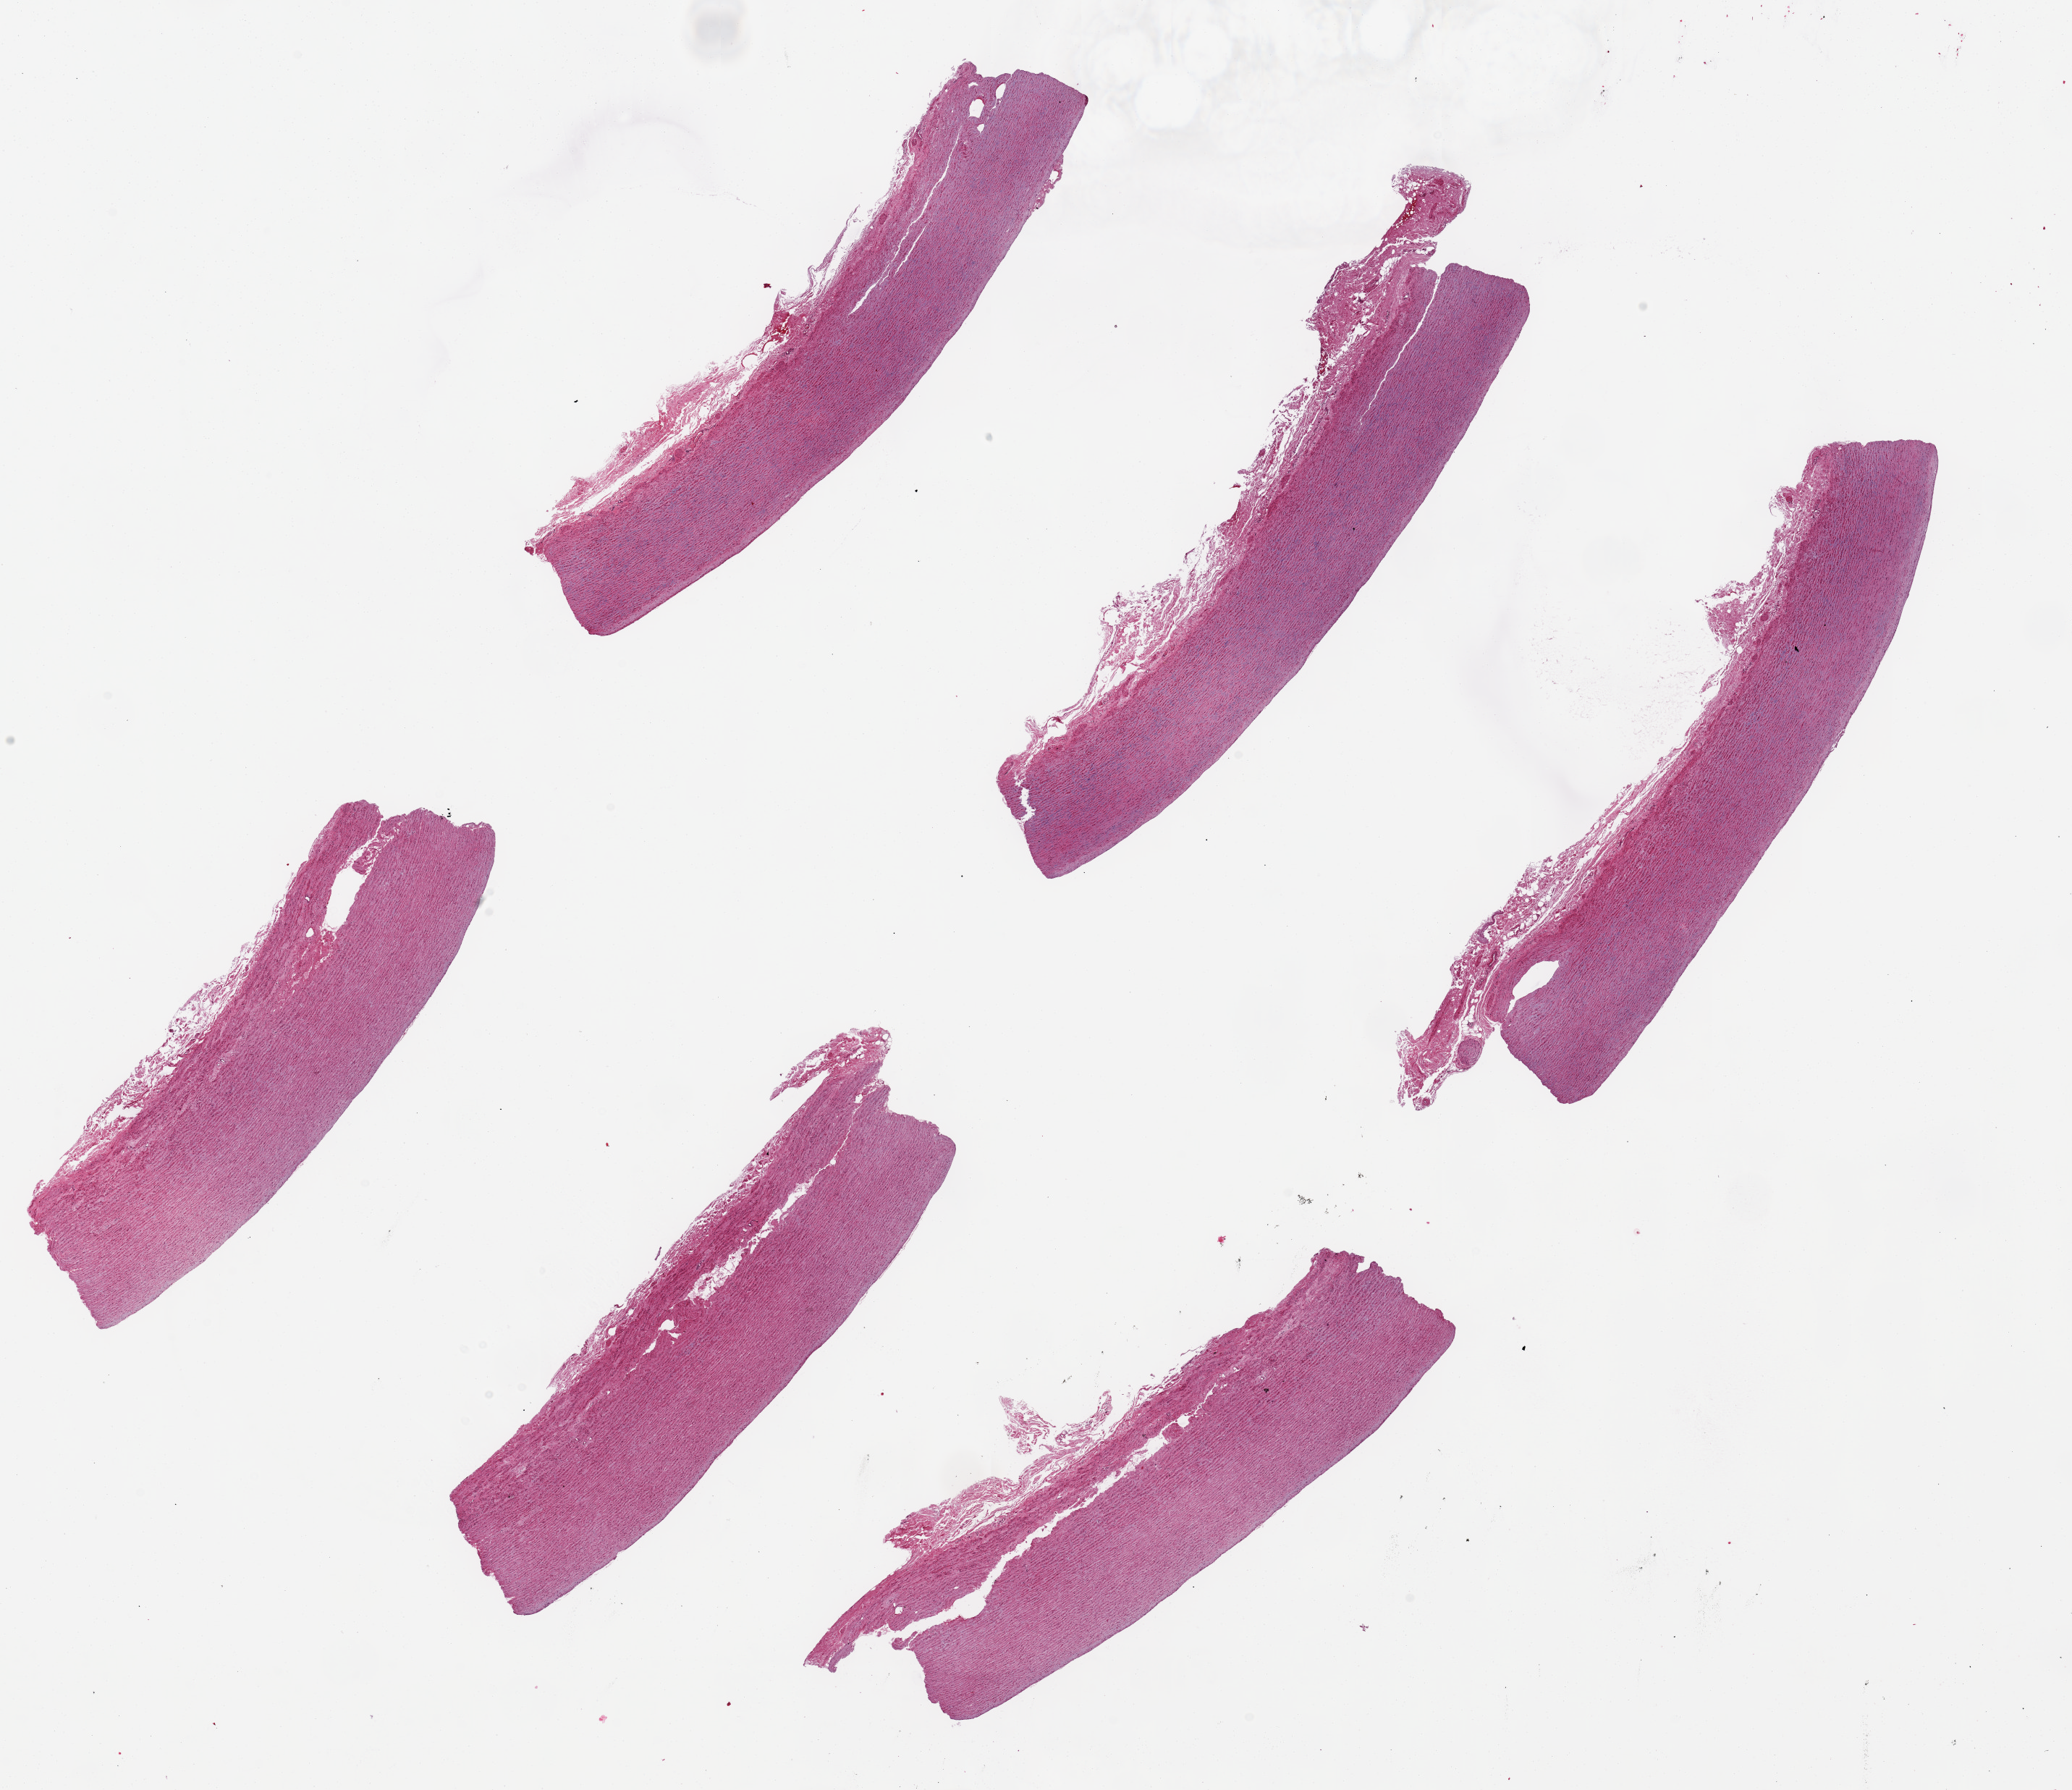
Digitized H&E-stained section, brightfield, a low-resolution overview of the entire scanned area, about 22.6 x 19.6 mm. PAXgene-fixed paraffin-embedded (PFPE) section. Section of aorta (target tissue). Donor tissue sample. Male donor.
Review note (as recorded): 6 pieces up to 8x2 mm.